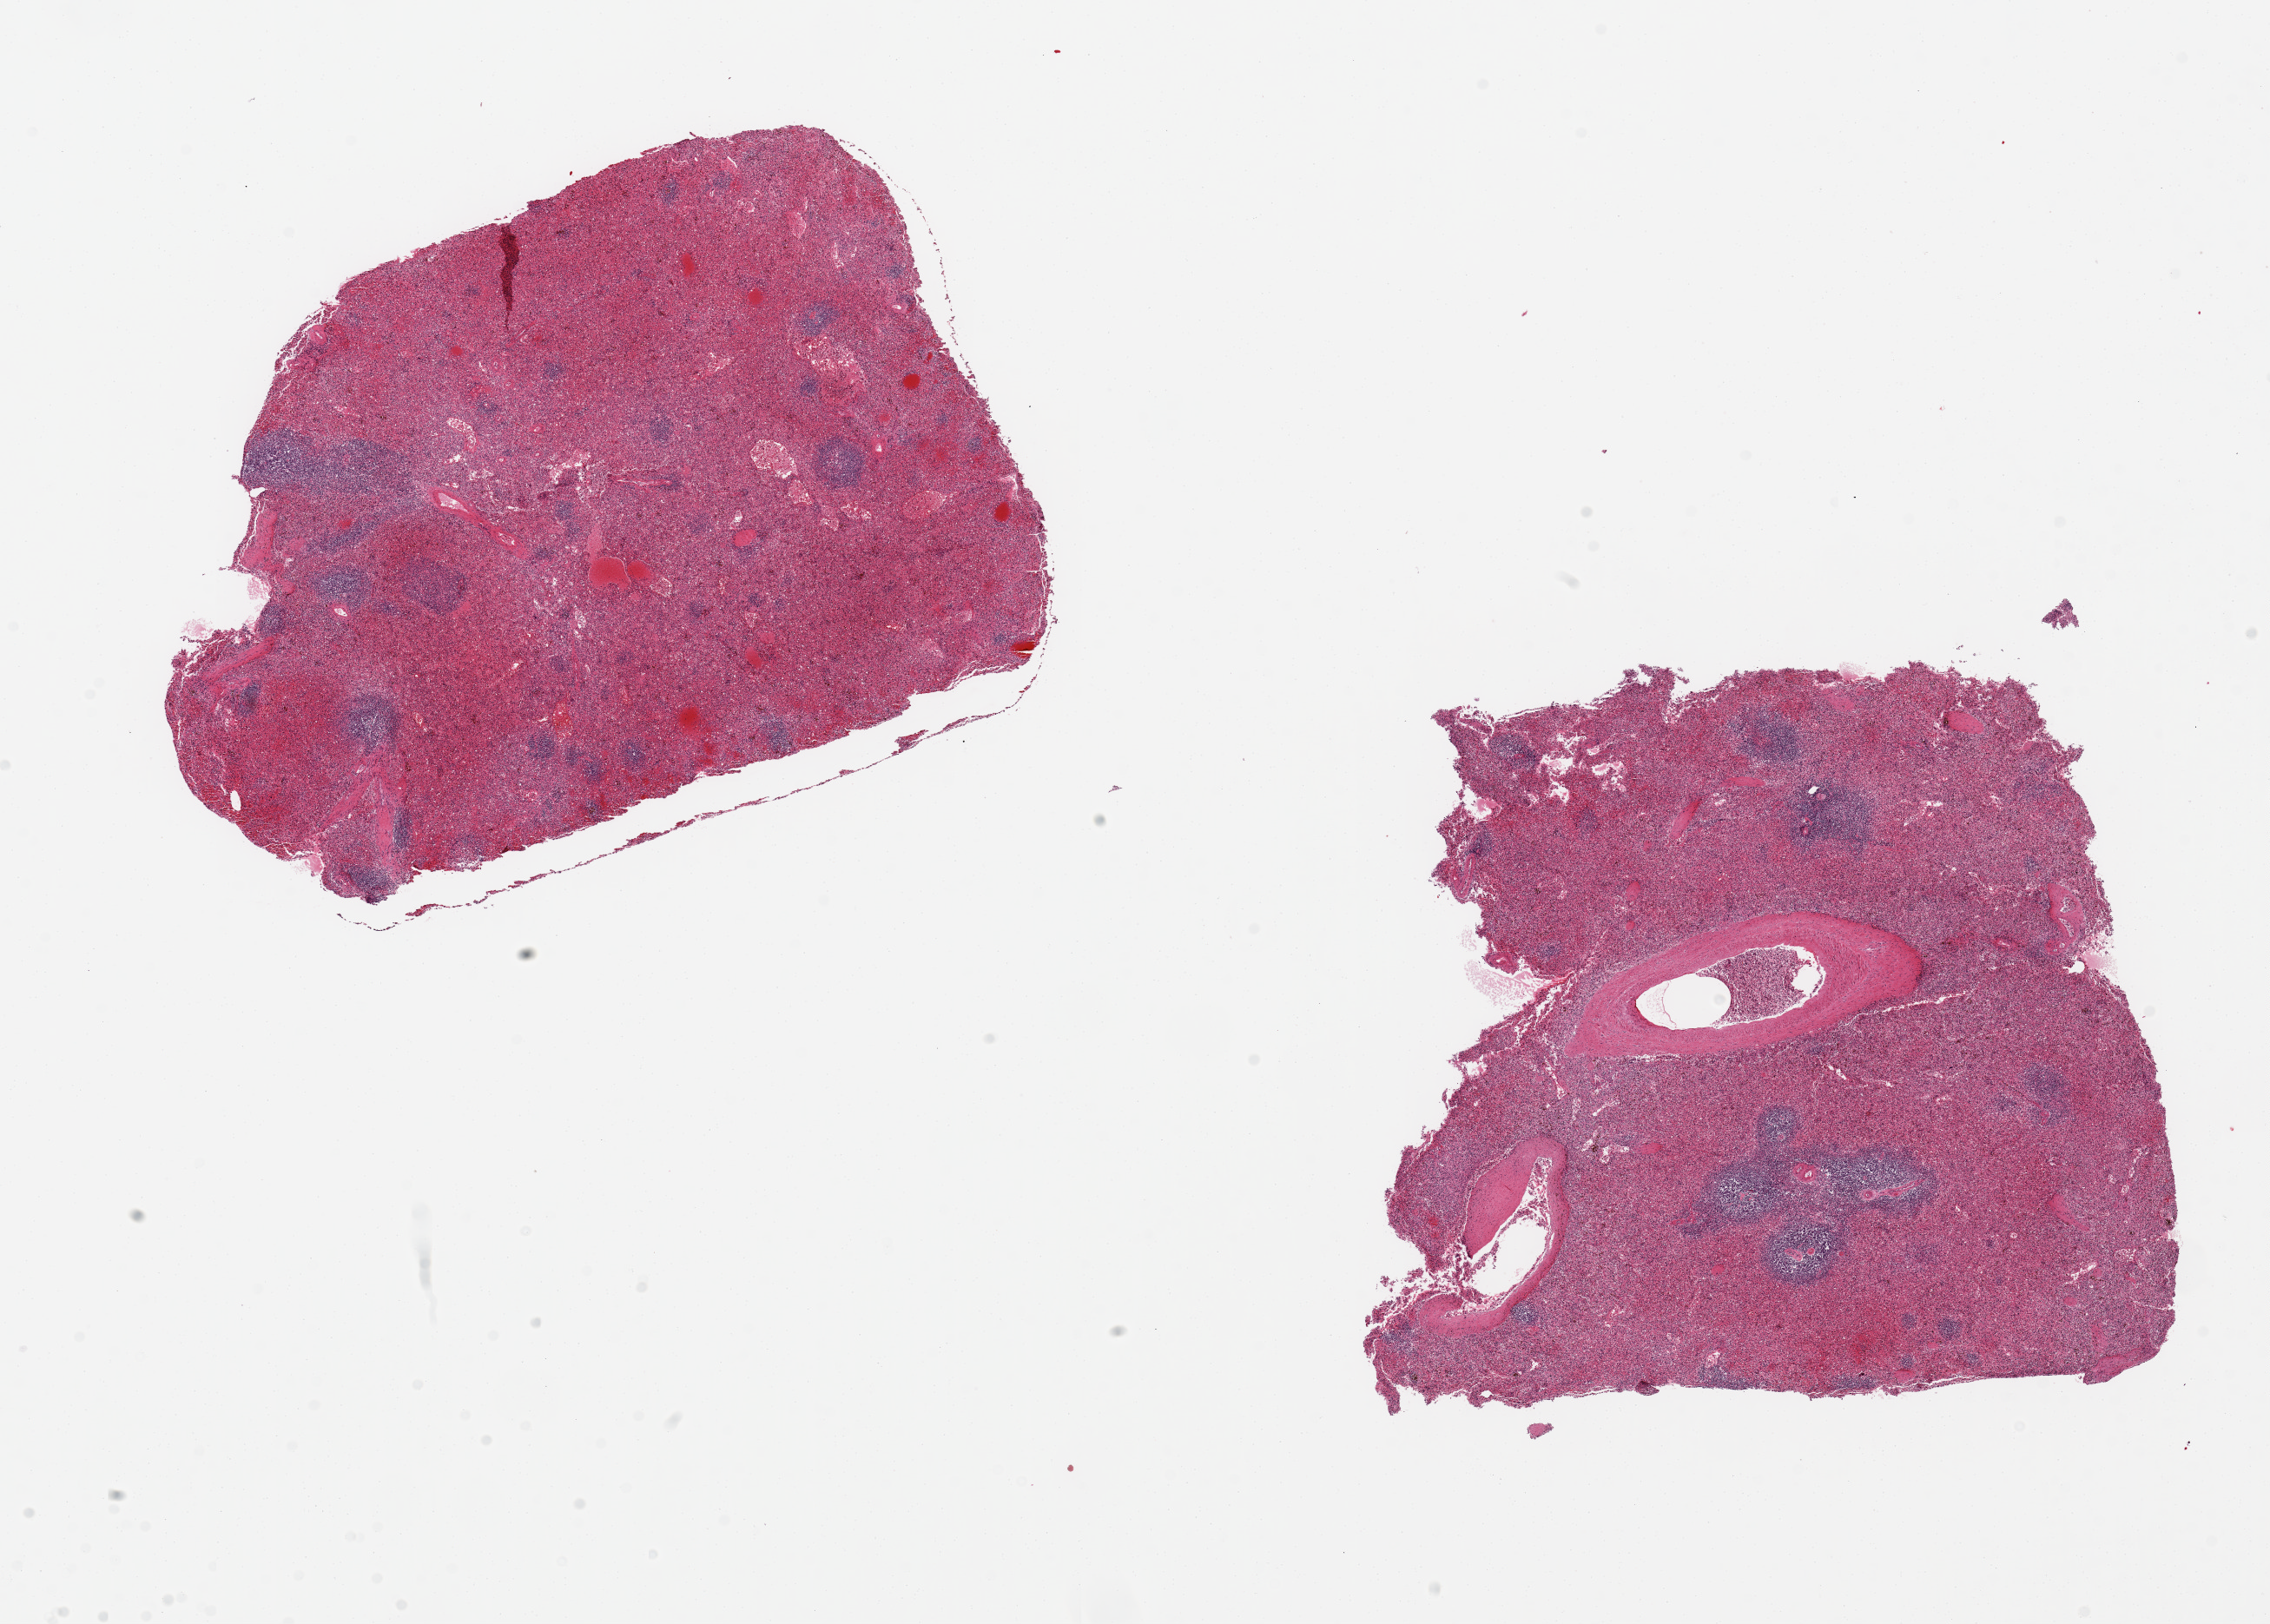
Hematoxylin and eosin (H&E) whole-slide image, brightfield — whole scanned area (about 20.7 x 14.8 mm, acquisition: 20x scan) shown as a low-resolution overview; PAXgene-fixed, paraffin-embedded tissue; sampled site (target tissue): spleen; tissue donor sample. Donor: male.
- review note (as recorded): 2 pieces 8x6 & 8x7mm